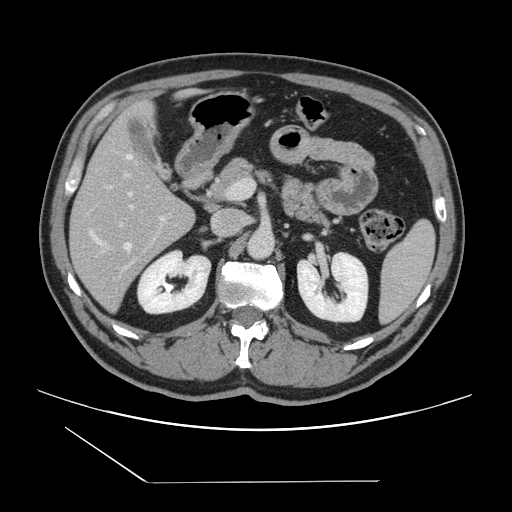
Contrast-enhanced abdominal CT, one axial slice. Slice 73 of 157 in the series (ordered by position). 120 kVp. Intravenous contrast given. Soft-tissue window (W 400 / L 40 HU). 2.5 mm slice thickness. 512 × 512 image matrix, field of view 407 × 407 mm. Male patient, age 61 years. Case-level facts recorded for this patient, not image findings: diagnosis: colorectal cancer liver metastases, imaged before liver resection; multiple liver metastases: yes; largest metastasis: 5.5 cm; disease in both lobes: yes.
Outlined on this slice (outlined manually by an expert reader):
- hepatic veins: bounding box [x1, y1, x2, y2] px = [89, 155, 132, 250]
- liver: [71, 103, 194, 310]
- planned liver remnant (the part of the liver to remain after resection): [72, 103, 195, 220]
- portal vein (with intrahepatic branches): [120, 173, 166, 265]